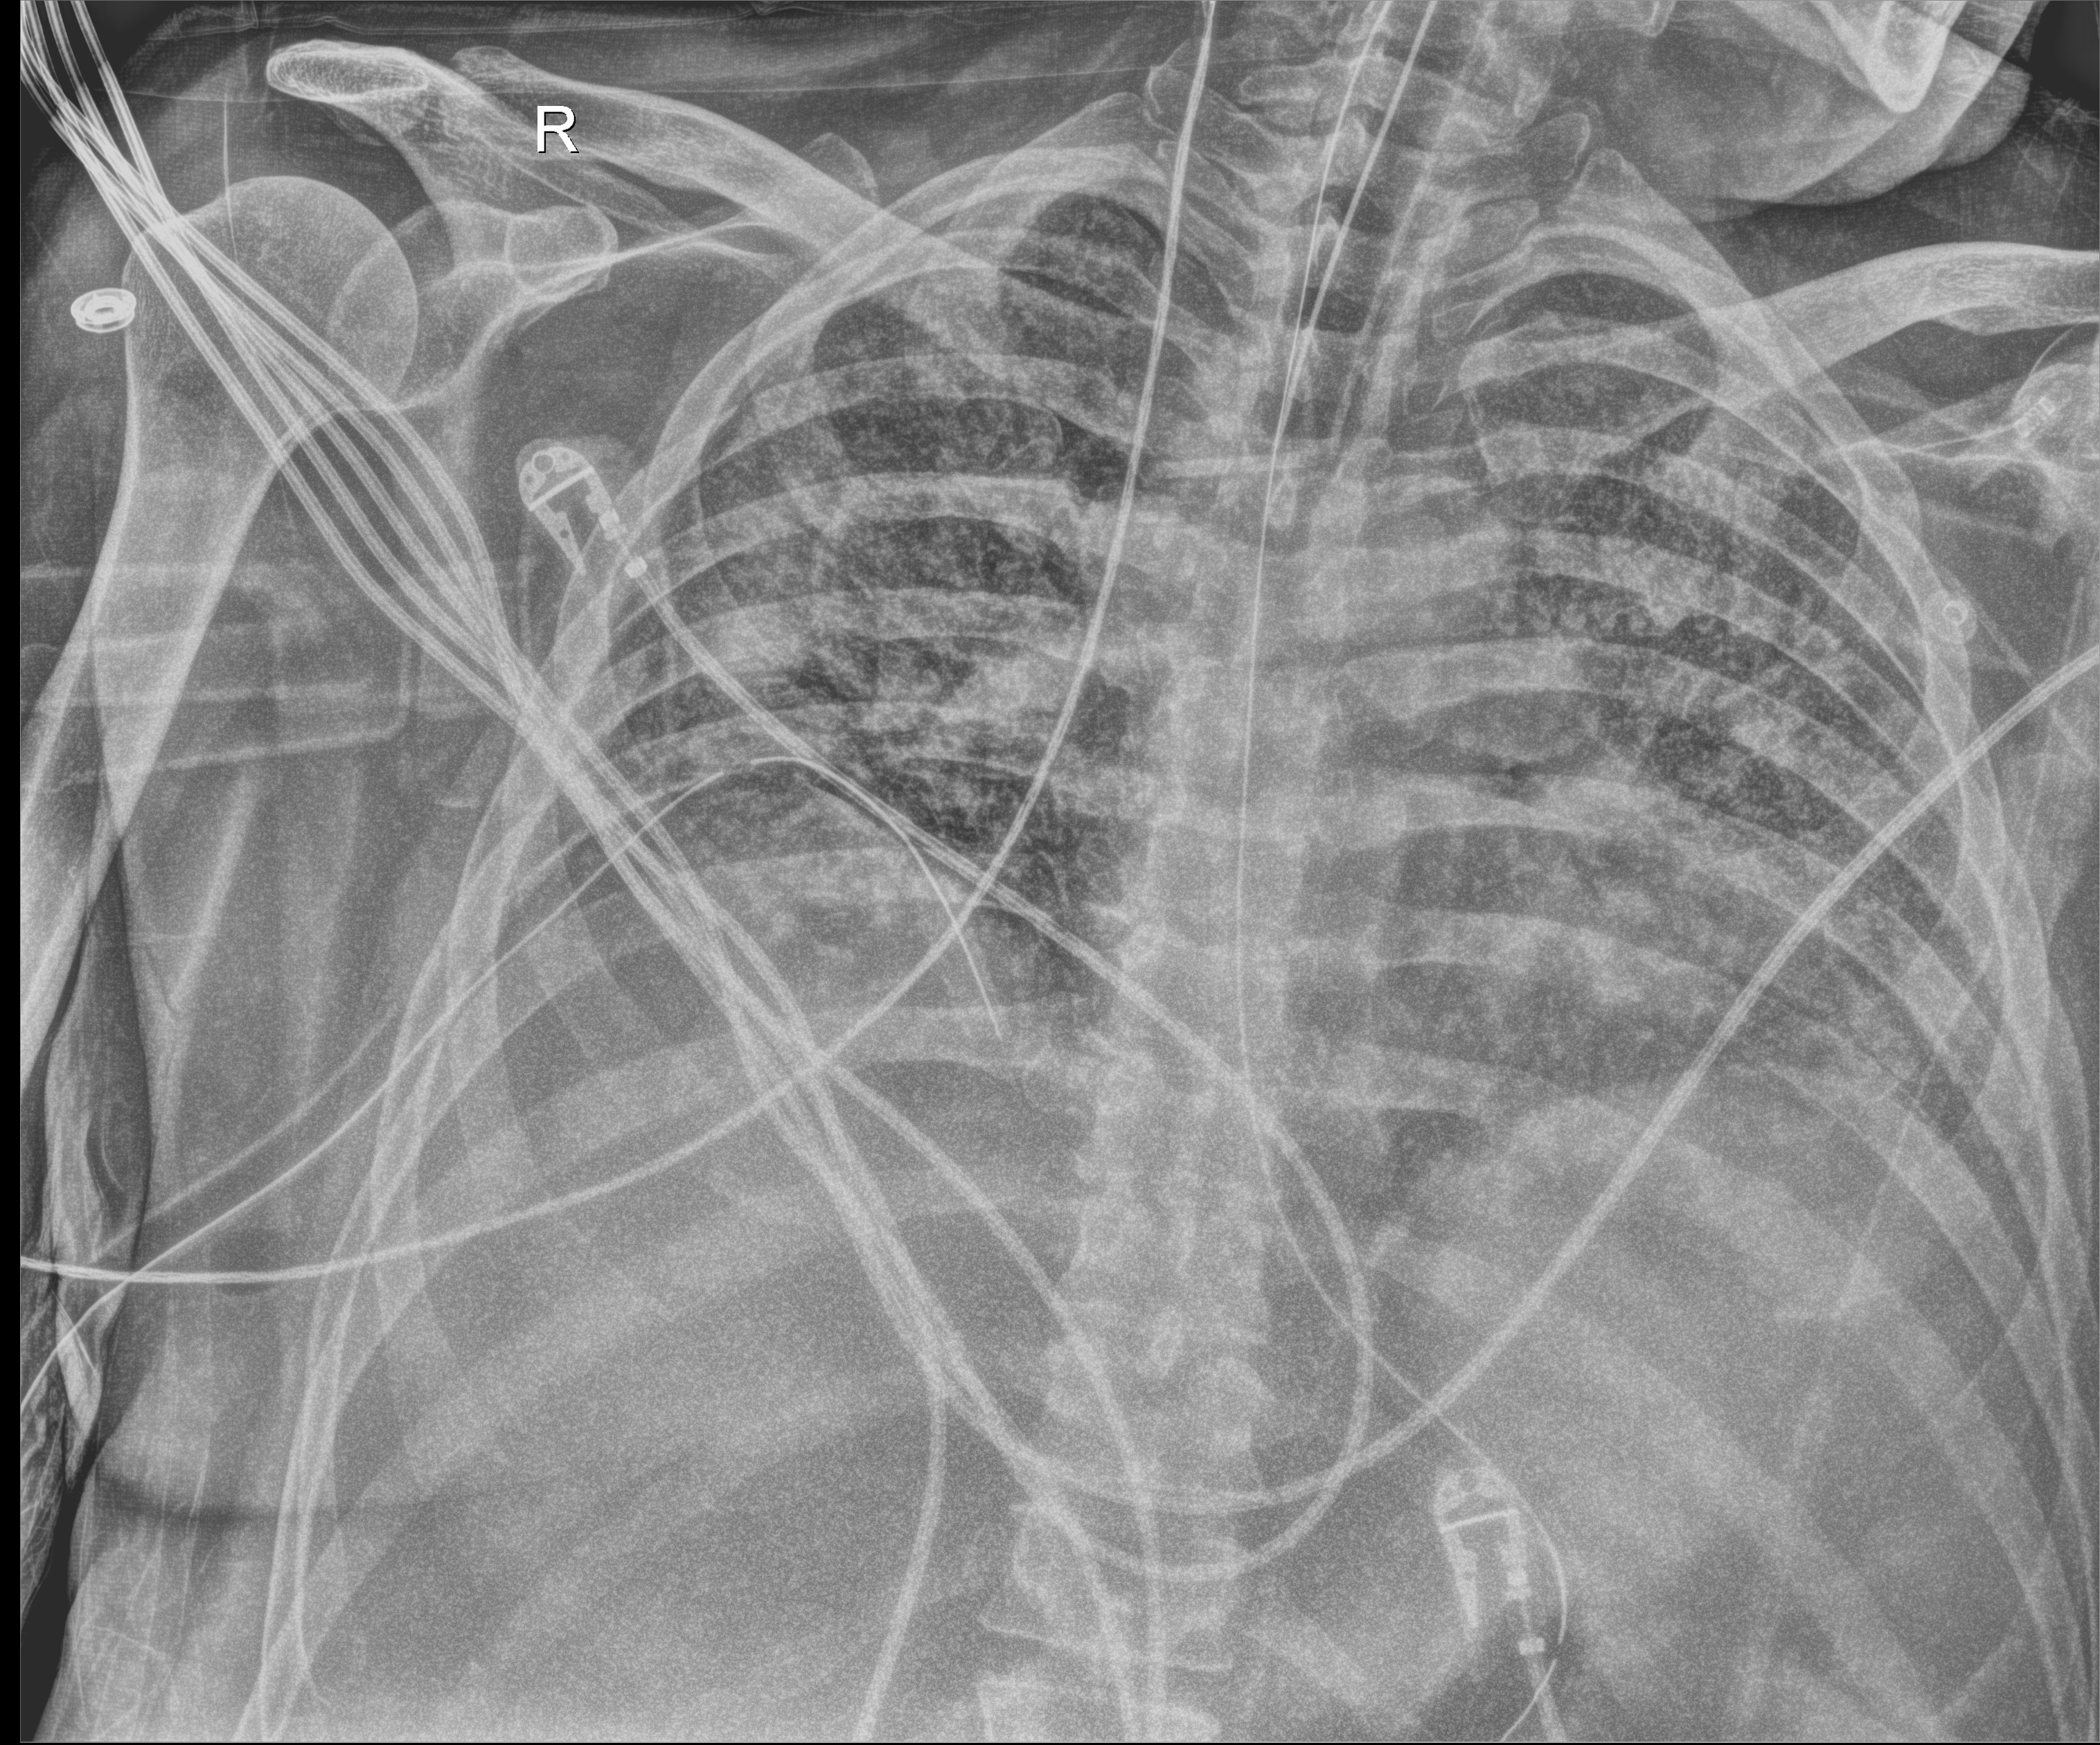
Portable chest radiograph; anteroposterior (AP) projection. Male patient hospitalised with COVID-19, age 18–59 years.
Admission-level facts for this patient (not findings on this image; timing relative to this image not recorded): mechanically ventilated during this hospital stay: yes; admitted to intensive care during this hospital stay: yes.